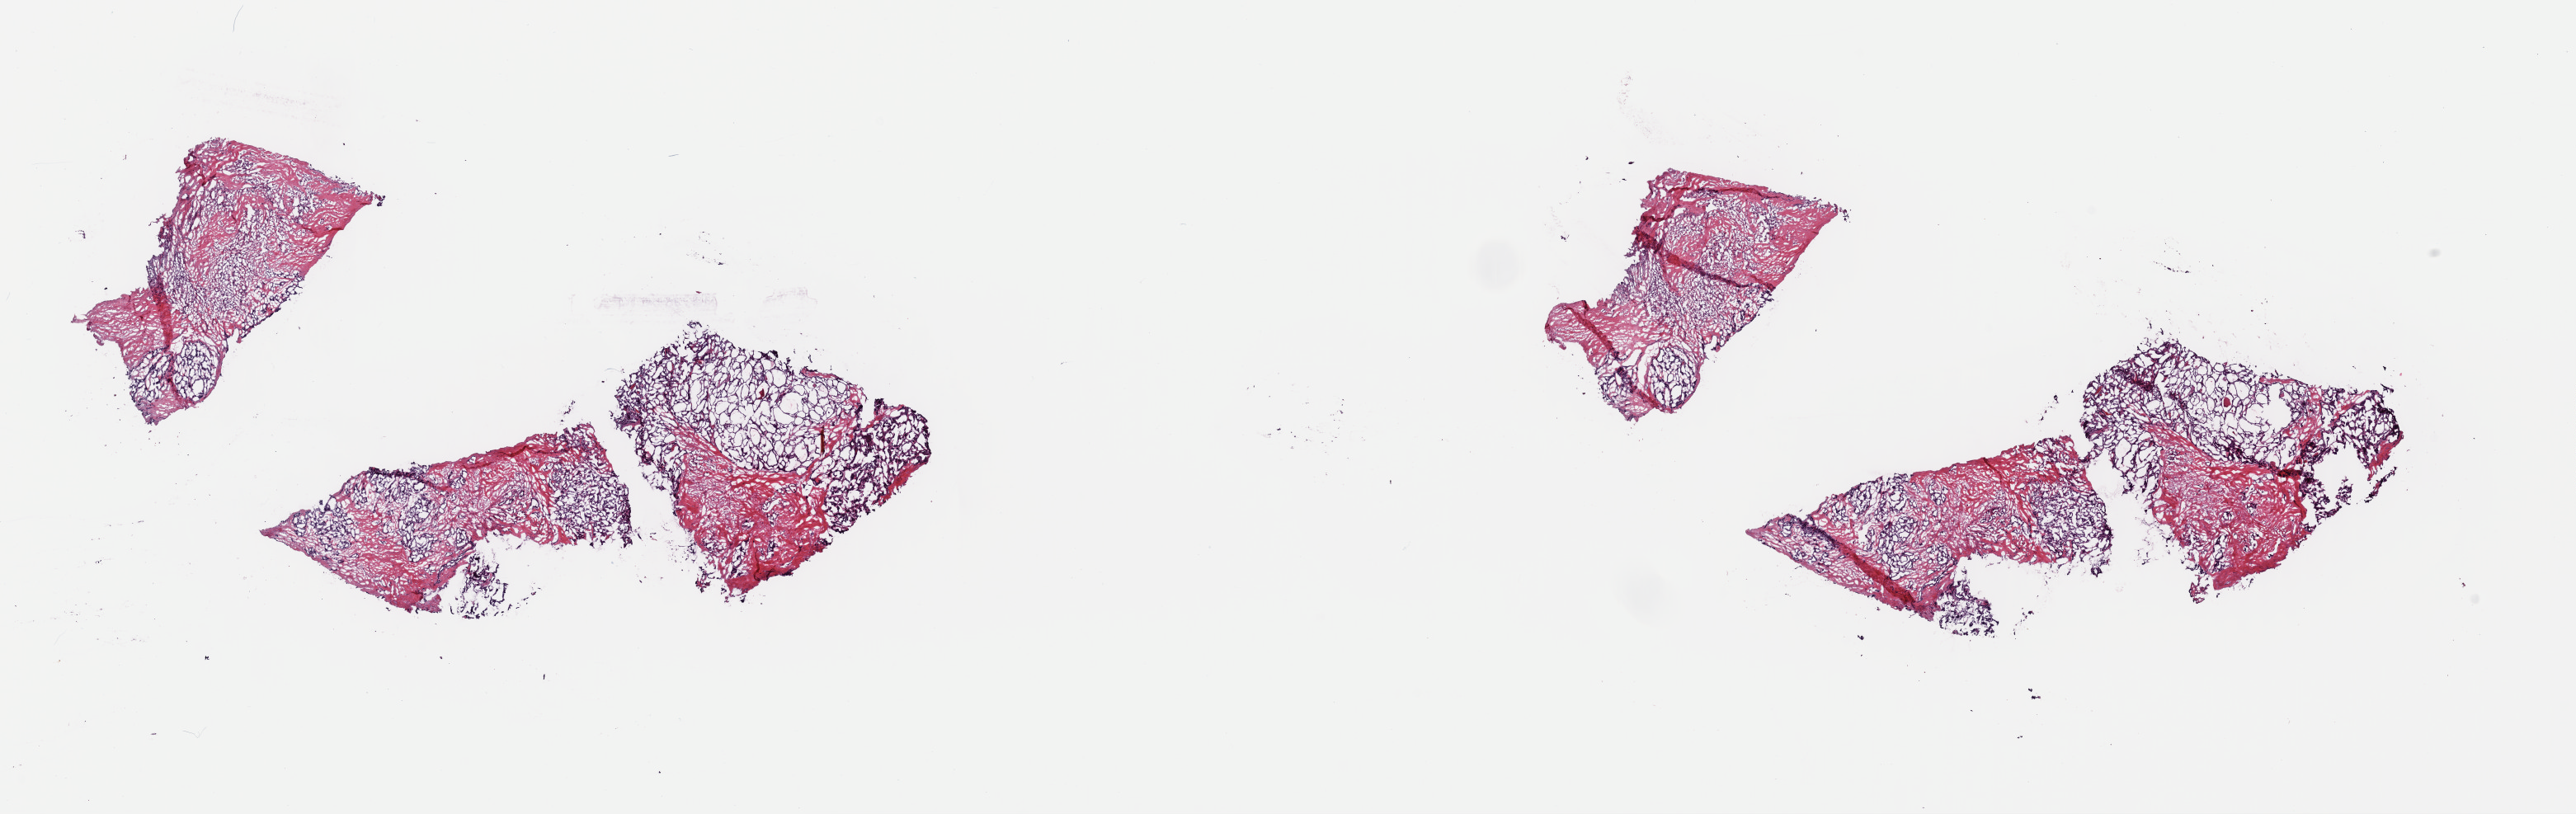
Digitized H&E tissue section (whole slide) — shown as a low-resolution overview of the whole scanned area (about 24.7 x 7.8 mm, from a 40x scan). Frozen section from the top of the tissue portion. Sample: primary tumour, thyroid. Female, age 78 years at initial diagnosis.
Histologic diagnosis: Papillary adenocarcinoma, NOS (thyroid gland).